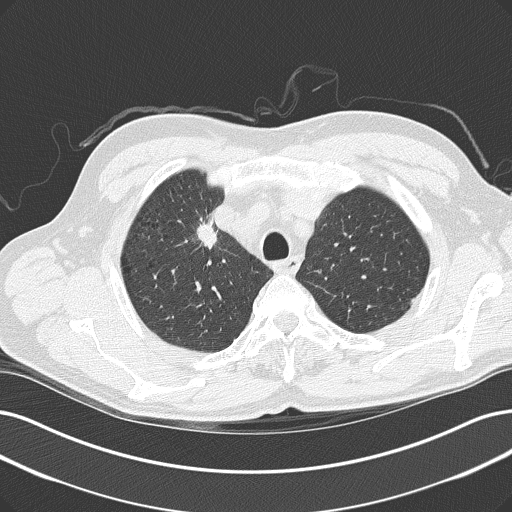
Low-dose screening chest CT, axial slice, baseline annual screen, lung window (W 1500 / L -600 HU), 2 mm slice thickness, lung (sharp) reconstruction kernel (B50f), 512 × 512 image matrix. Male, age 61 years at enrolment. Current smoker at enrolment.
- Lesion marked by an expert reader, bounding box (x1, y1, x2, y2) in pixels: (189, 219, 246, 266).
- The screening reader recorded 2 non-calcified nodules or masses ≥4 mm on this exam (right upper lobe, right upper lobe); which of them this box marks is not recorded.
- Official screen result: positive, change unspecified: nodule(s) >= 4 mm or enlarging nodule(s), mass(es), or other non-specific abnormalities suspicious for lung cancer.
- Lung cancer was diagnosed 54 days after this screen: adenocarcinoma, NOS, right upper lobe, poorly differentiated (G3), stage IIIB (AJCC 6th edition).